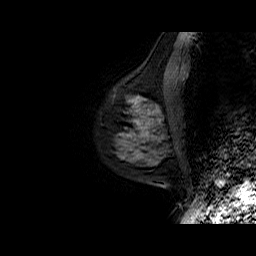
Breast MRI (dynamic contrast-enhanced), one sagittal slice. Position 17 of 50 along the scan axis. Dynamic contrast-enhanced series, time point 2 of 6 at this slice position (early post-contrast). 1.5 T. TE 6.5 ms, TR 32.9 ms. 4 mm slice thickness. 256 × 256 image matrix. Female patient. Case-level facts recorded for this patient, not image findings: setting: breast cancer imaged before/during neoadjuvant chemotherapy; receptor status: HR-positive, HER2-negative.
Outlined on this slice (semi-automatically segmented with operator editing):
- analysis volume of interest (the breast-tissue region the enhancement analysis was run in; not a lesion): box from (x=116, y=75) to (x=179, y=149) px
- tumour enhancement mask (voxels above the 100 % enhancement threshold inside the analysis volume of interest): (x=135, y=102)–(x=150, y=125)